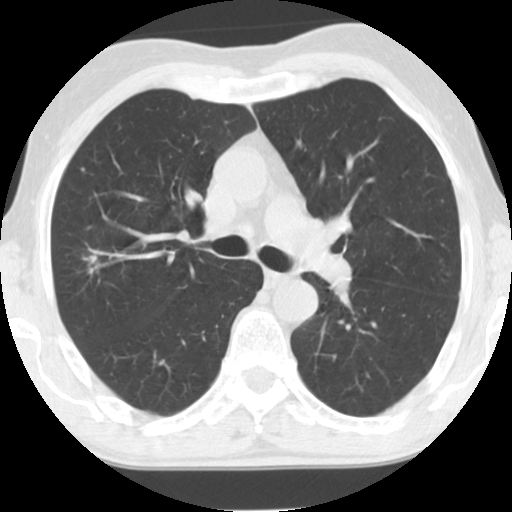
Low-dose screening chest CT, one axial slice; slice 81 of 124 in the series (ordered by position); 120 kVp; lung window (W 1500 / L -600 HU); 2.5 mm slice thickness; 512 × 512 image matrix, field of view 310 × 310 mm.
Outlined on this slice (outlined manually by an expert reader):
- lesion 1 (tumor, upper lobe of right lung): bounding box <86,254,98,270> (left, top, right, bottom; pixels)